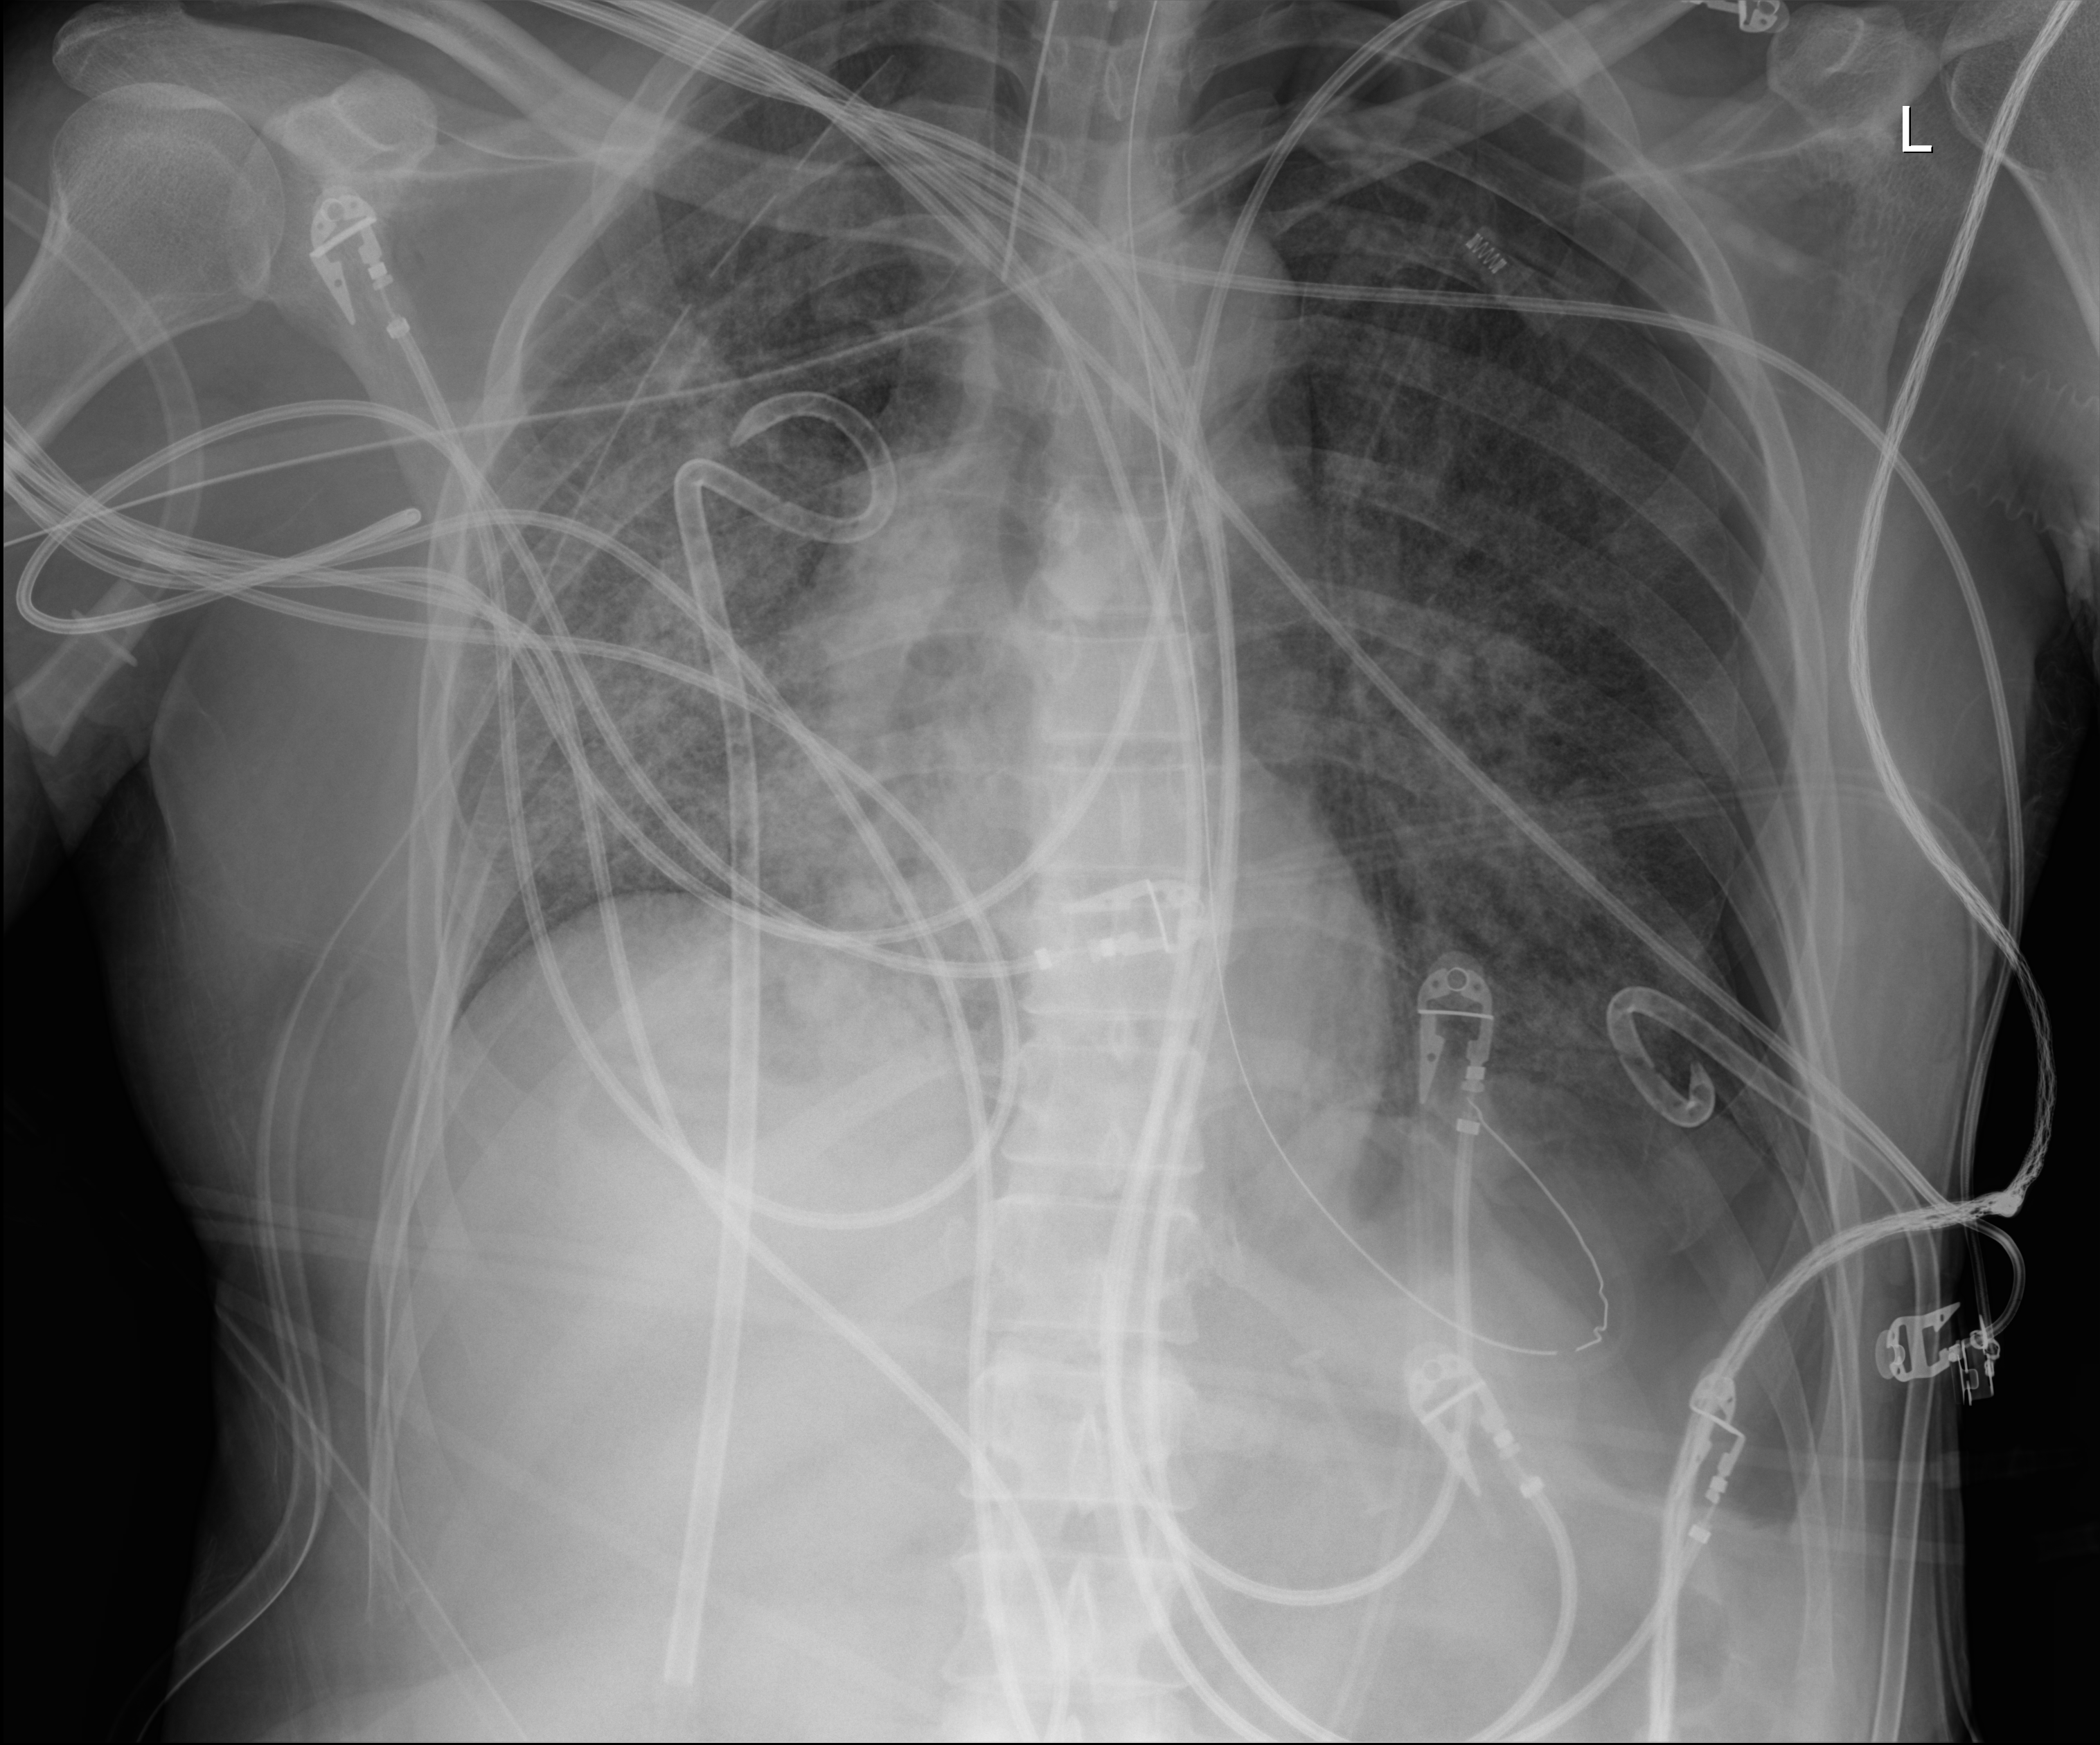
Chest radiograph (digital radiography). Adult patient hospitalised with COVID-19, age 18–59 years.
Admission-level facts for this patient (not findings on this image; timing relative to this image not recorded):
- mechanically ventilated during this hospital stay: yes